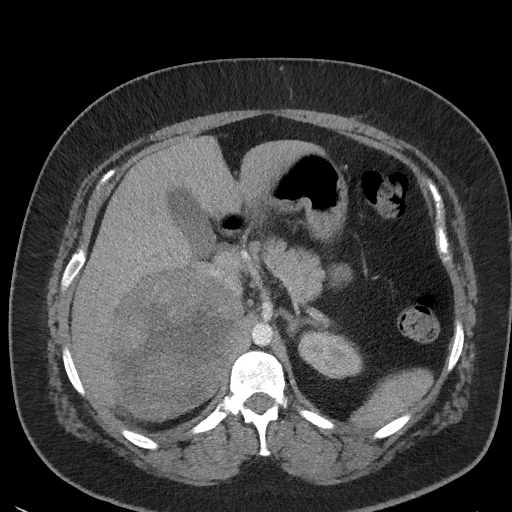
Contrast-enhanced abdominal CT, one axial slice. Slice 33 of 56 in the series (ordered by position). Reconstruction kernel I41f/3. Soft-tissue window (W 400 / L 40 HU). 5 mm slice thickness. 512 × 512 image matrix, field of view 373 × 373 mm. Female patient, age 35 years. Case-level facts recorded for this patient, not image findings: diagnosis: adrenocortical carcinoma; tumour side: right adrenal; tumour size at pathology: 15 cm; Ki-67 index: 40 %.
Annotated regions visible in this slice (semi-automatically segmented with operator editing):
- mass: box from (x=112, y=271) to (x=234, y=415) px